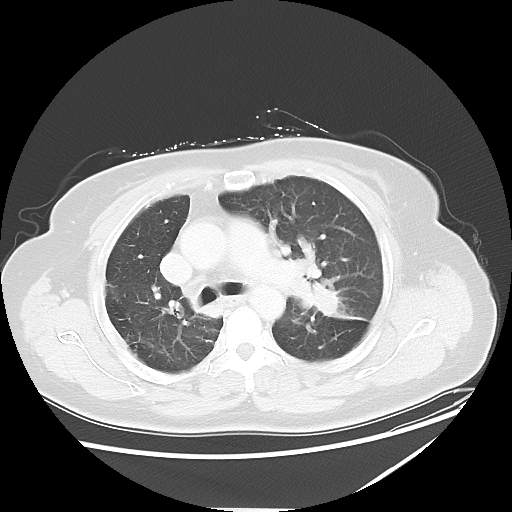
Chest CT, one axial slice. Slice 37 of 54 in the series (ordered by position). Reconstruction kernel LUNG. 120 kVp. Lung window (W 1500 / L -600 HU). 5 mm slice thickness. 512 × 512 image matrix, field of view 384 × 384 mm. Patient: female, 61 years. From the clinical record (not read from this slice): clinical TNM (as recorded): T1c N3 M1.
Outlined on this slice (rectangle marked by the reading radiologist):
- lung tumour (recorded histology: adenocarcinoma): bounding box <305,277,369,325> (left, top, right, bottom; pixels)